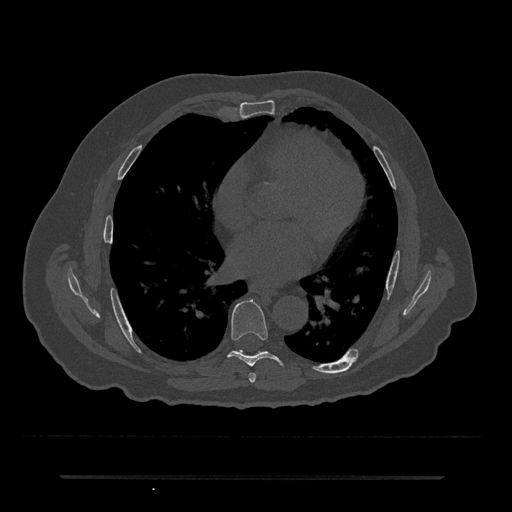
CT including the spine, one axial slice. Position 381 of 797 along the scan axis. Reconstruction kernel Br40s/3. Bone window (W 1800 / L 400 HU). 0.5 mm slice thickness. 512 × 512 image matrix, field of view 437 × 437 mm. Patient: male, 69 years. Case-level facts recorded for this patient, not image findings: primary cancer: prostate.
Outlined on this slice (semi-automatically segmented with operator editing):
- T6 vertebra: bounding box <249,373,256,382> (left, top, right, bottom; pixels)
- T7 vertebra: <228,299,286,366>